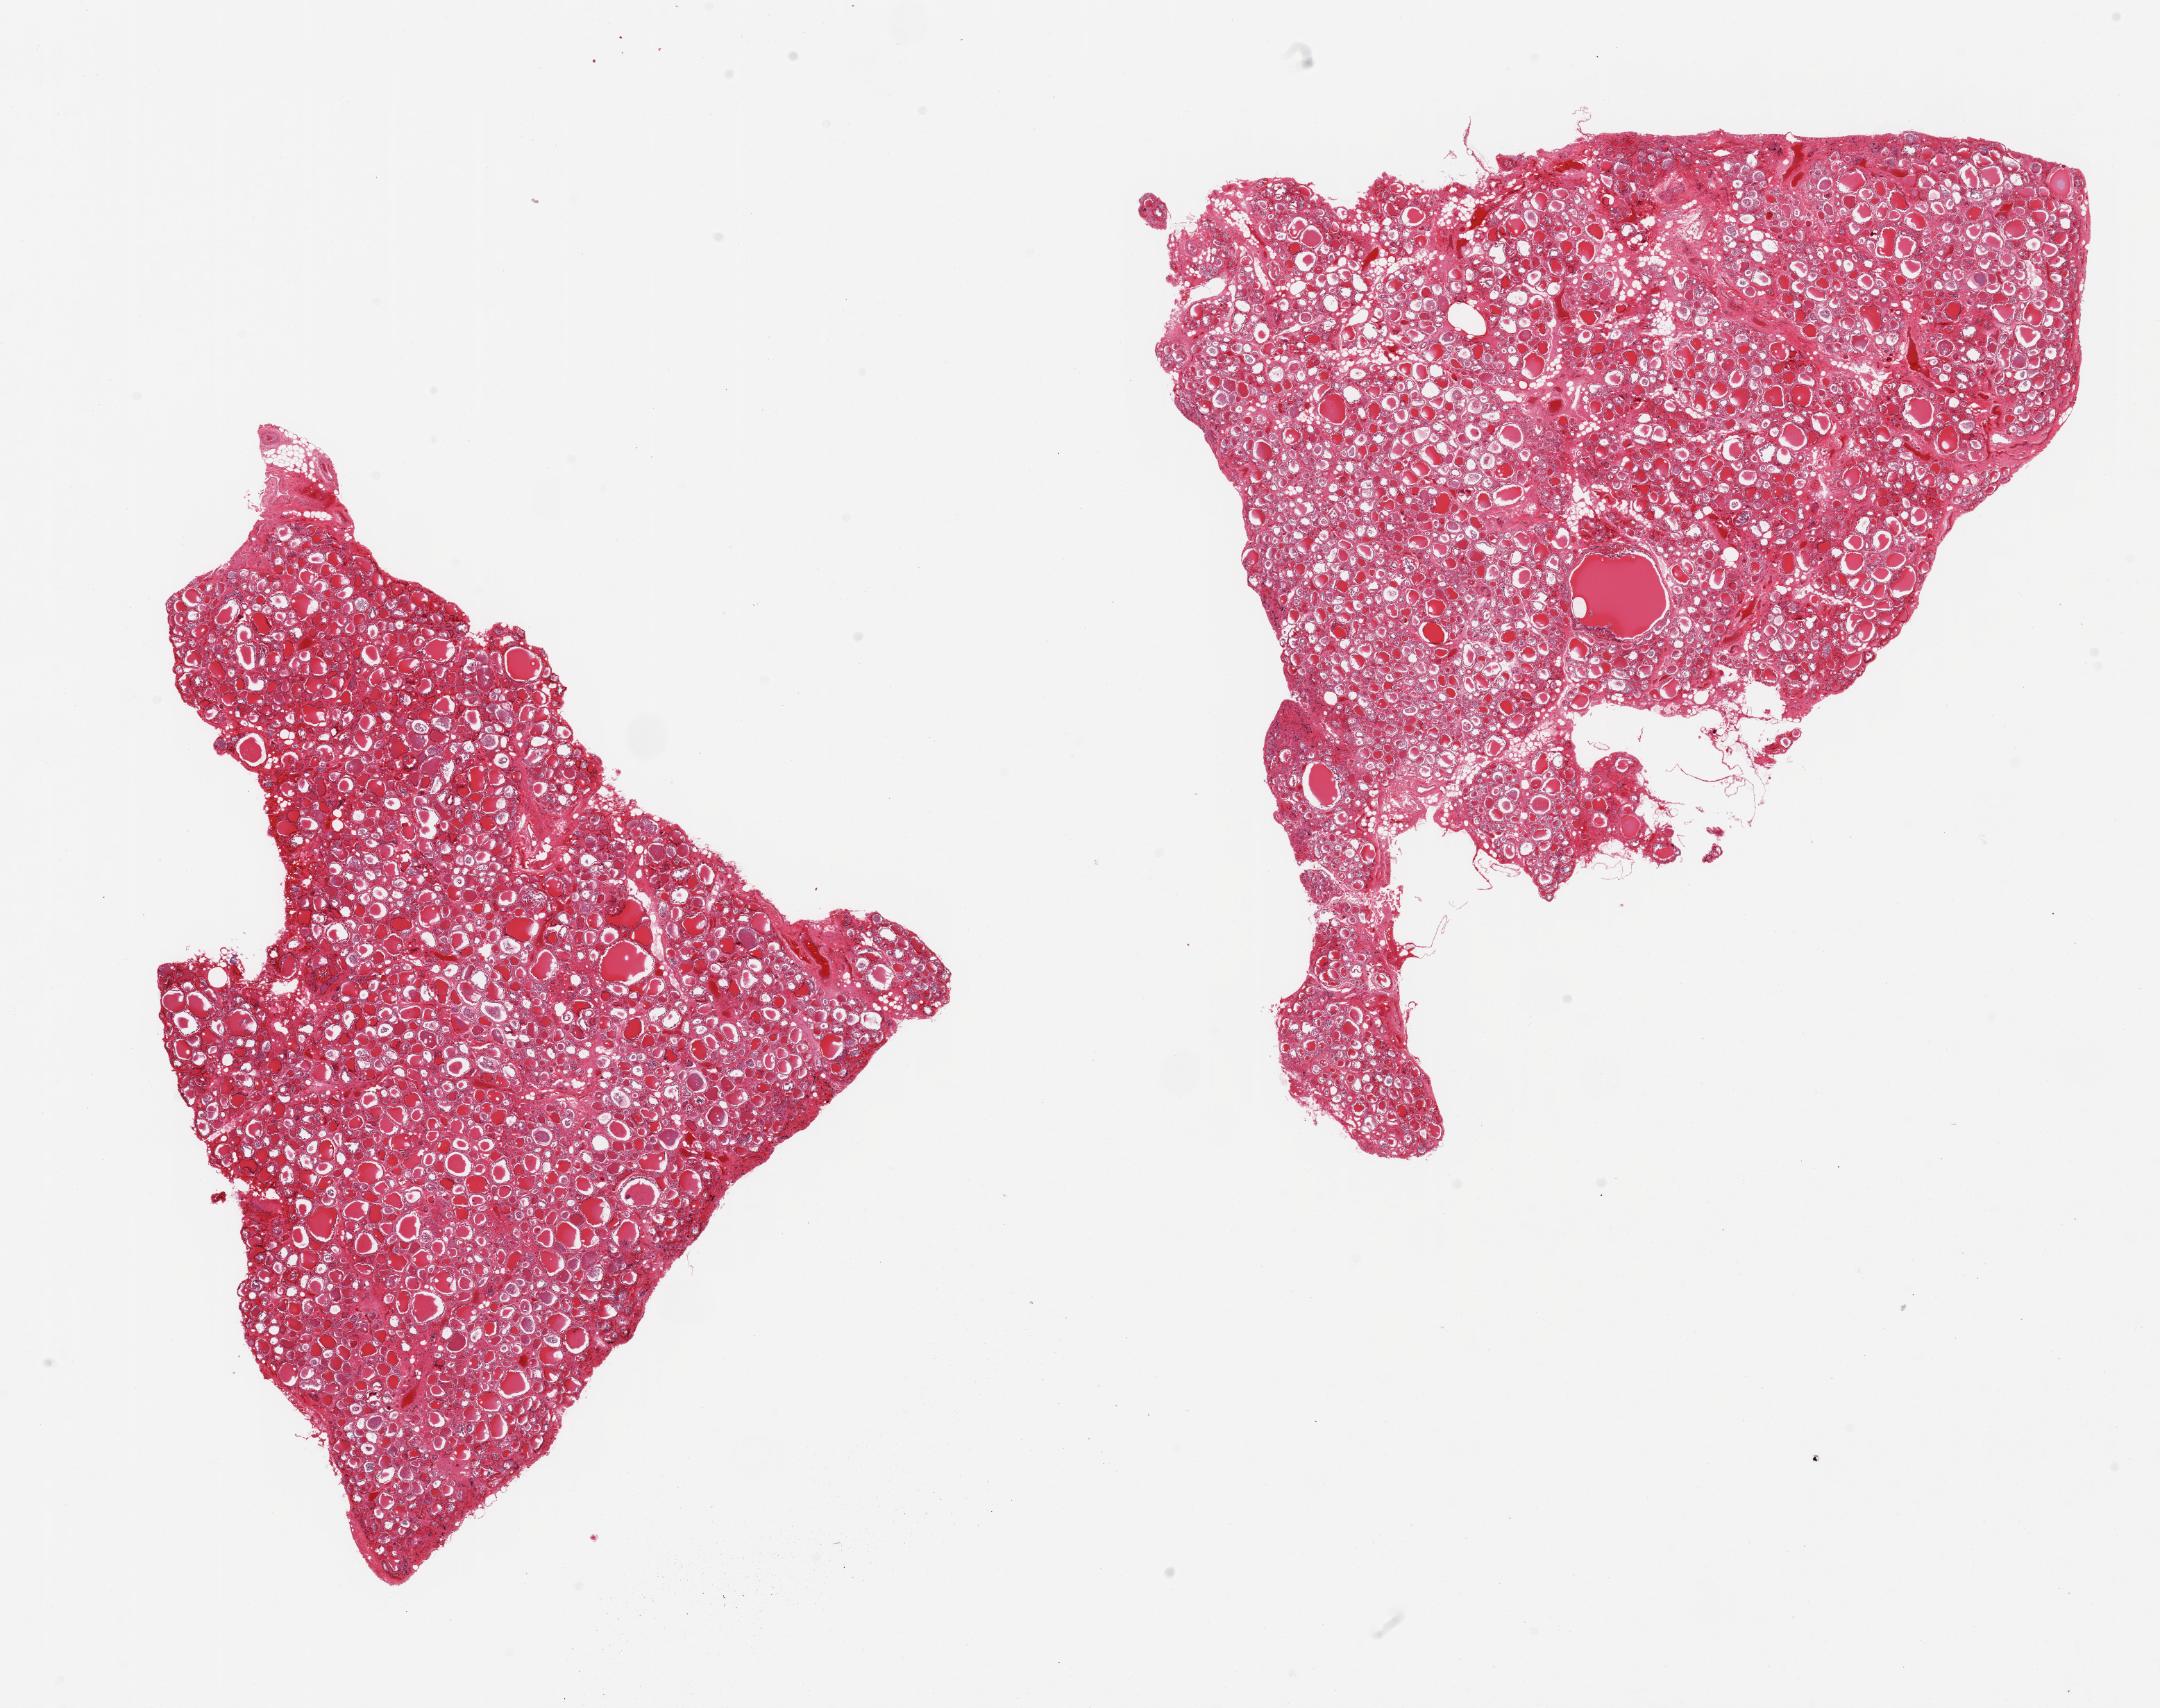
Whole-slide image, H&E stain — shown as a low-resolution overview of the whole scanned area (about 24.6 x 19.5 mm, acquisition: 20x scan). PAXgene-fixed paraffin-embedded (PFPE) section. Section of thyroid (target tissue). Tissue donor sample. Donor sex: male.
Reviewer comment on this tissue sample: 2 pieces.